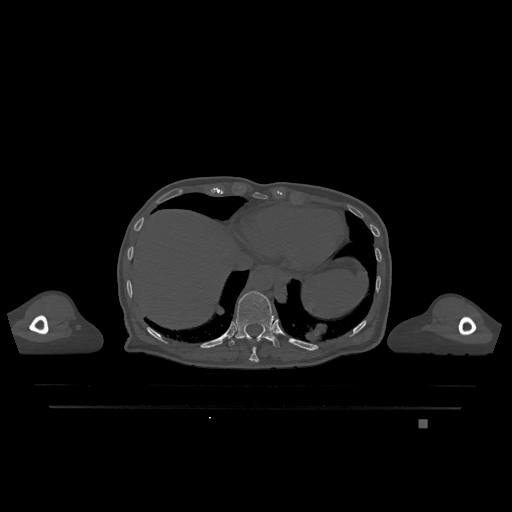
CT including the spine, one axial slice; slice 605 of 1317 in the series (ordered by position); bone window (W 1800 / L 400 HU); 512 × 512 image matrix, field of view 500 × 500 mm. Female patient, age 74 years. Case-level facts recorded for this patient, not image findings: primary cancer: lung.
Annotated regions visible in this slice (semi-automatic segmentation, software-assisted and operator-edited):
- T10 vertebra: bounding box <249,347,259,362> (left, top, right, bottom; pixels)
- T11 vertebra: <228,291,280,347>